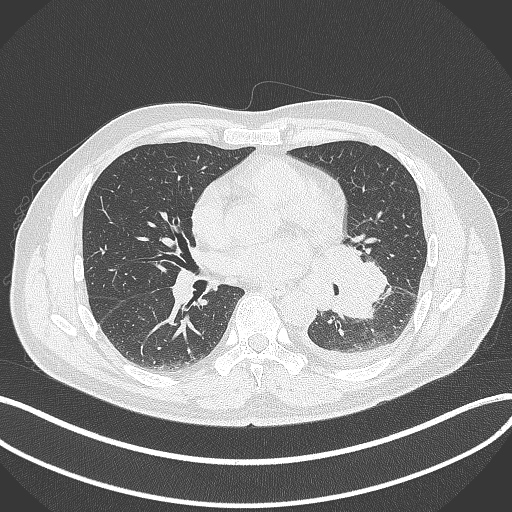
Chest CT, one axial slice; position 175 of 342 along the scan axis; reconstruction kernel B70f; lung window (W 1500 / L -600 HU); 1 mm slice thickness; 512 × 512 image matrix, field of view 400 × 400 mm. Male patient, age 58 years. From the clinical record (not read from this slice): clinical TNM (as recorded): T3 N1 M1b; histopathological grade: G3.
Outlined on this slice (bounding box drawn by a radiologist):
- lung tumour (recorded histology: small cell carcinoma): box from (x=313, y=236) to (x=396, y=323) px